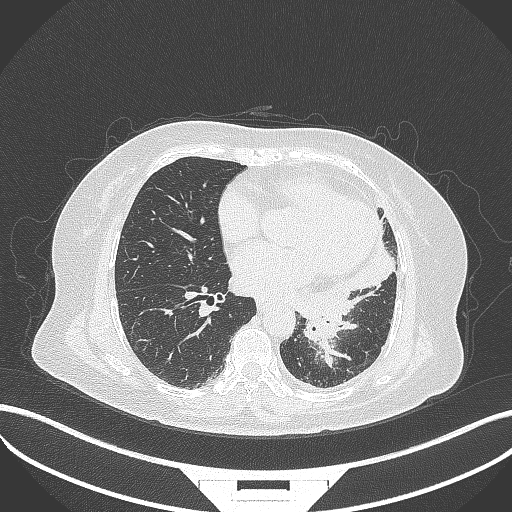
Chest CT, one axial slice; position 151 of 322 along the scan axis; reconstruction kernel B70f; 120 kVp; lung window (W 1500 / L -600 HU); 1 mm slice thickness; 512 × 512 image matrix, field of view 400 × 400 mm. Patient: female, 69 years. From the clinical record (not read from this slice): clinical TNM (as recorded): T2b N3 M1.
Structures marked on this image (rectangle marked by the reading radiologist):
- lung tumour (recorded histology: adenocarcinoma): bounding box <298,310,346,344> (left, top, right, bottom; pixels)